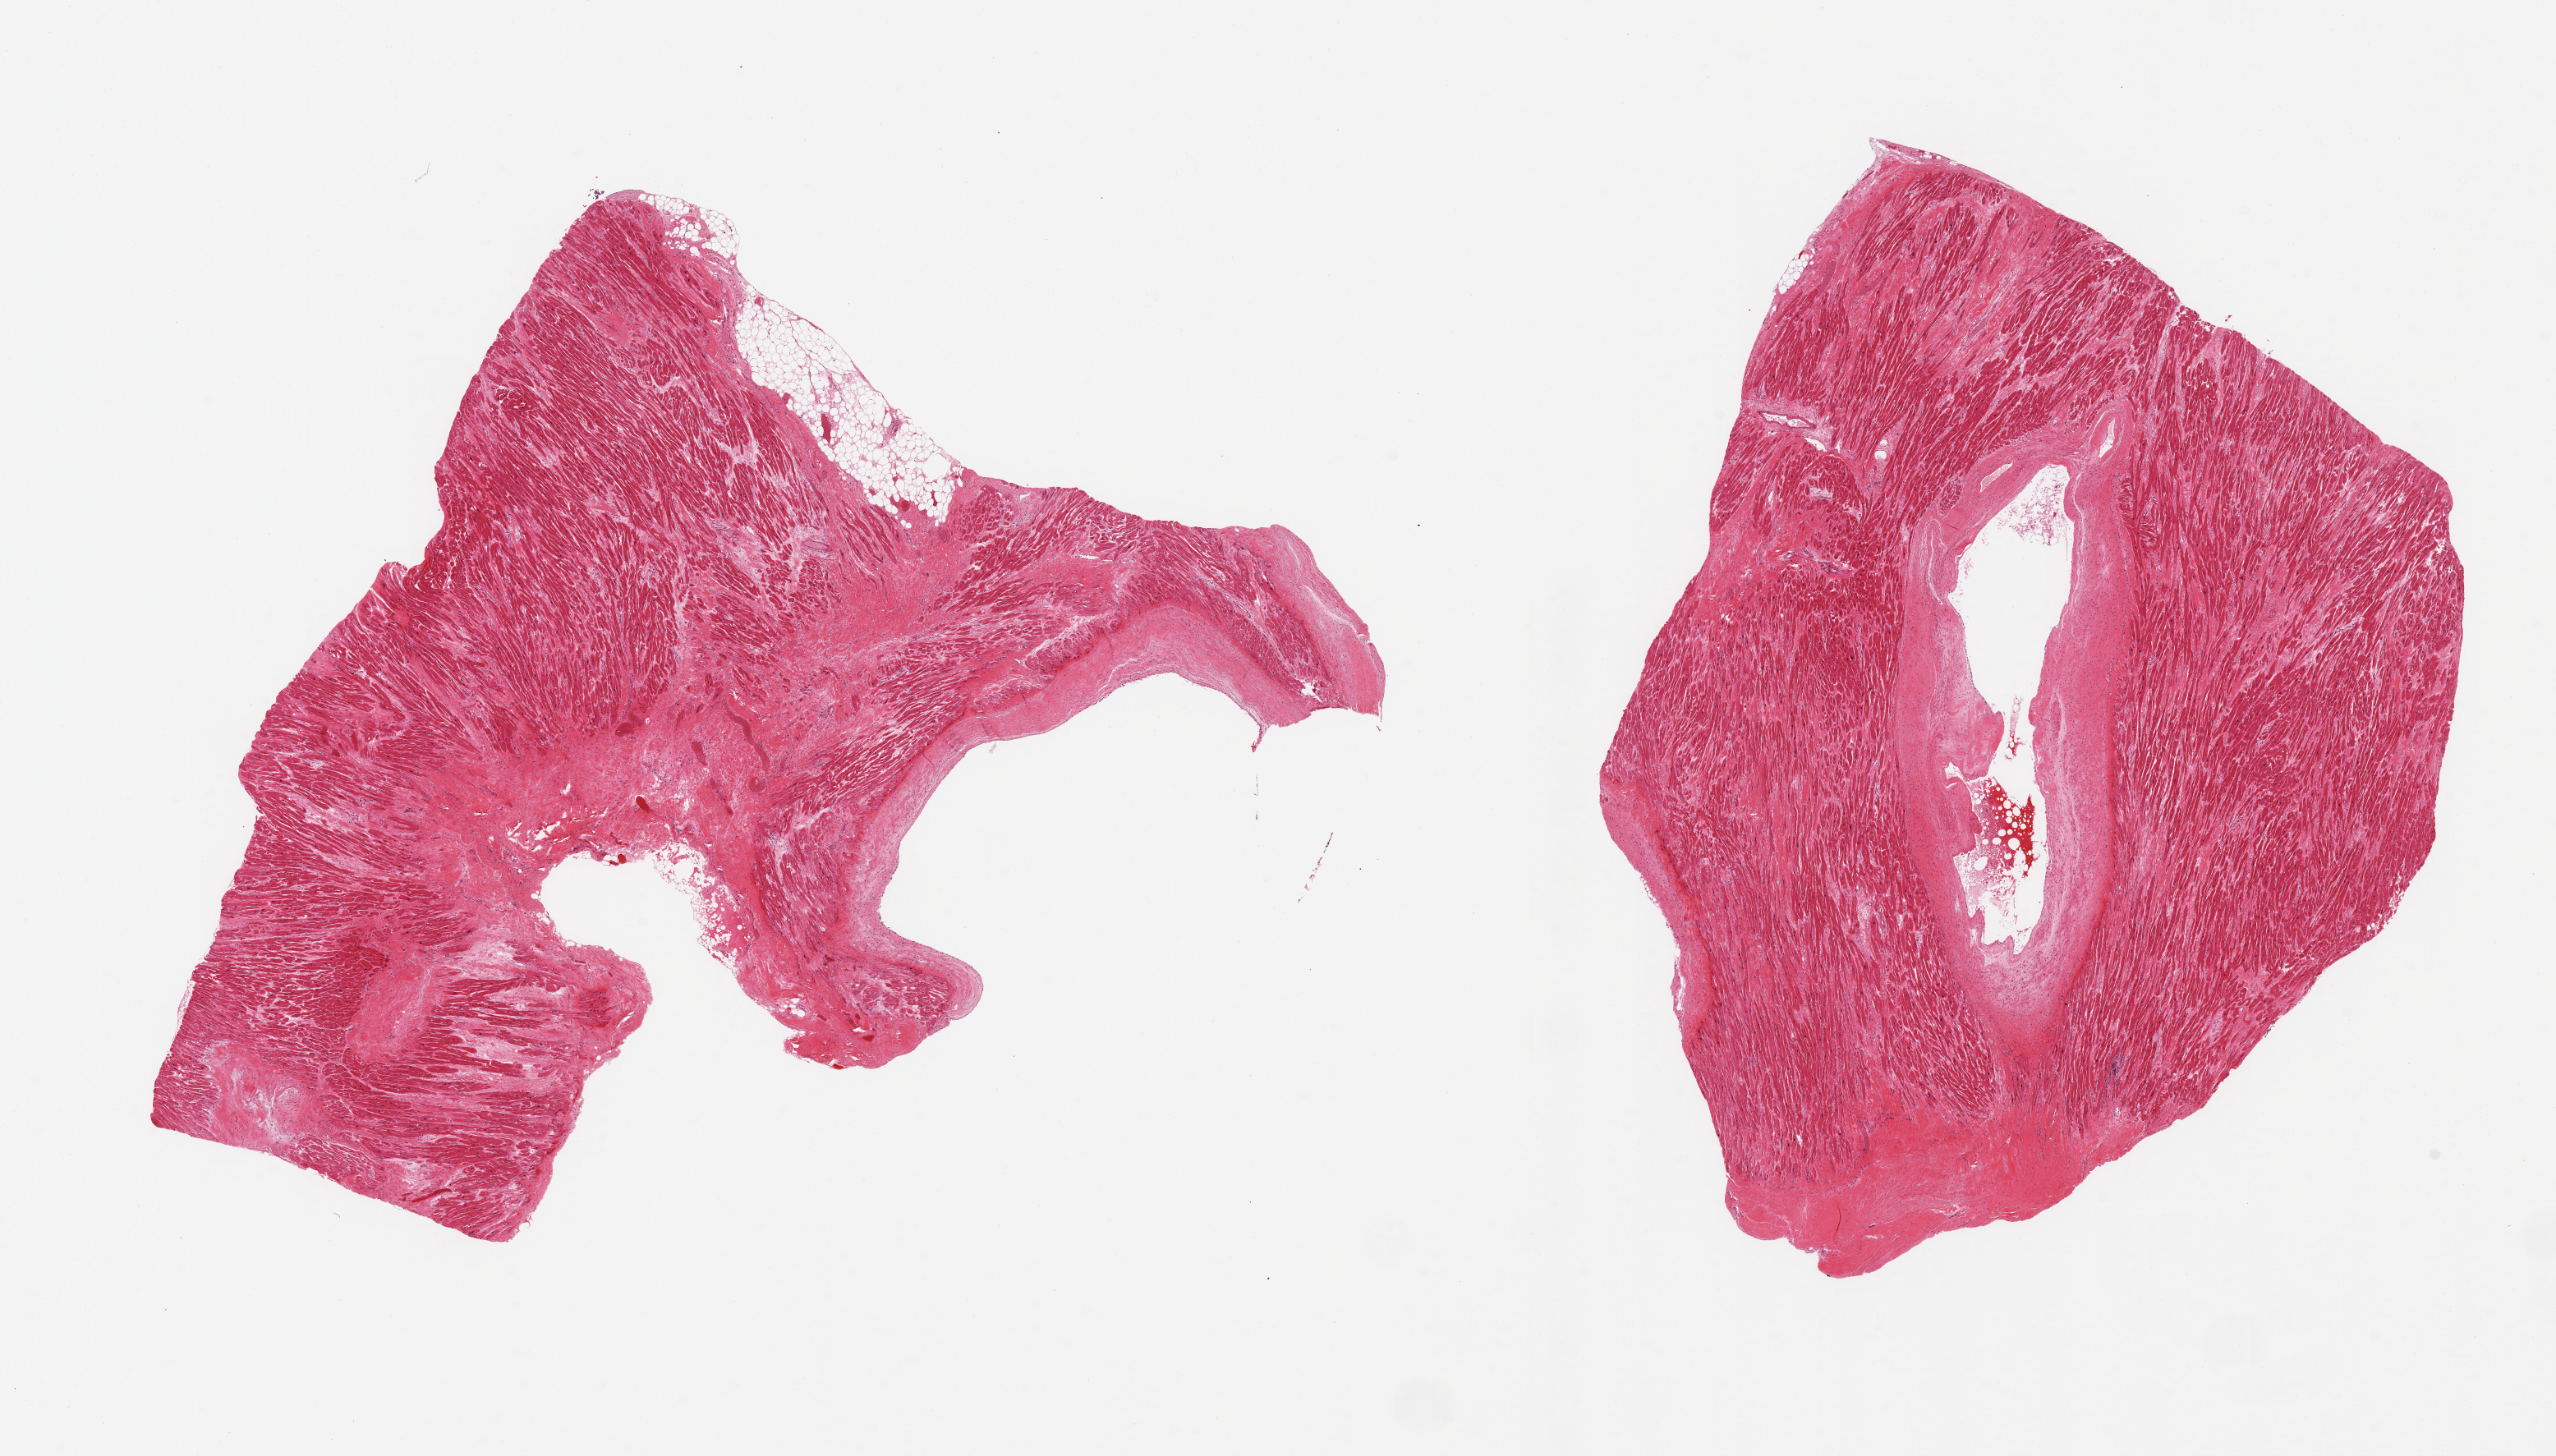
H&E whole-slide image — a low-resolution overview of the entire scanned area, about 24.6 x 14.0 mm. PAXgene-fixed, paraffin-embedded tissue. Sampled site (target tissue): heart. Donor tissue sample. Donor: male.
Reviewer comment on this tissue sample: 2 pieces, diffuse marked chronic ischemic damage, remote infarcts noted.